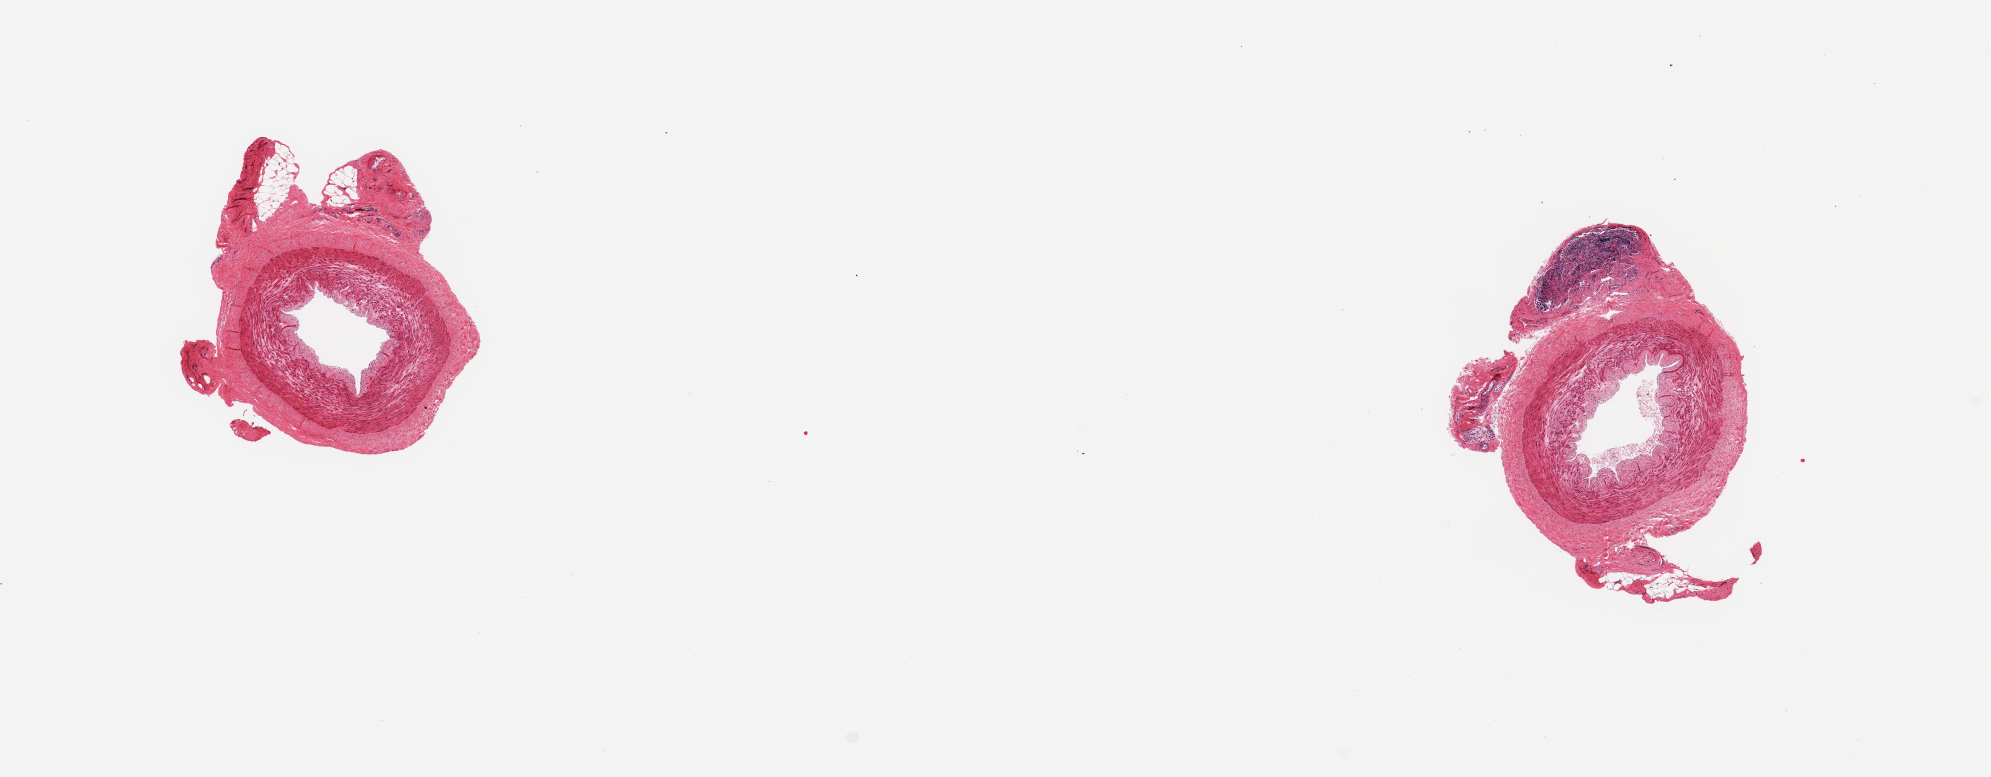
Haematoxylin and eosin whole-slide image, brightfield — shown as a low-resolution overview of the whole scanned area (about 15.8 x 6.1 mm, slide scanned at 20x), PAXgene-fixed, paraffin-embedded tissue, target tissue: tibial artery, donor tissue sample. Donor sex: female.
Pathologist's review note for this sample: 2 pieces; no lesions; up to 0.6 mm extraneous peripheral fibrovascular (1 lymphoid-rich) tissue.